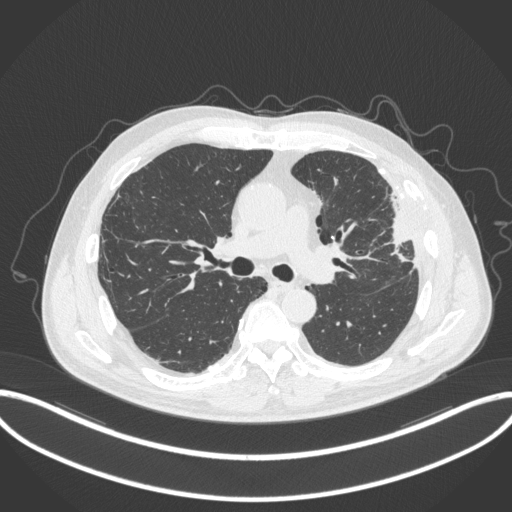
Chest CT, one axial slice; slice 206 of 382 in the series (ordered by position); reconstruction kernel B31f; 120 kVp; lung window (W 1500 / L -600 HU); 1 mm slice thickness; 512 × 512 image matrix, field of view 415 × 415 mm. Male patient, age 64 years. Case-level facts recorded for this patient, not image findings: clinical TNM (as recorded): T4 N1 M0; histopathological grade: G3.
Structures marked on this image (bounding box drawn by a radiologist):
- lung tumour (recorded histology: adenocarcinoma): bounding box <380,186,419,268> (left, top, right, bottom; pixels)